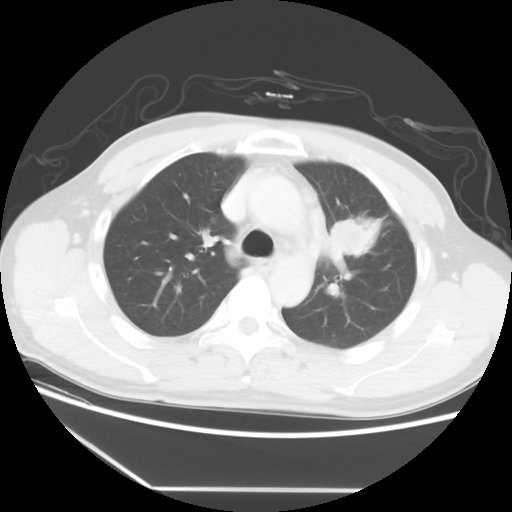
Chest CT, one axial slice. Slice 39 of 56 in the series (ordered by position). 120 kVp. Lung window (W 1500 / L -600 HU). 5 mm slice thickness. 512 × 512 image matrix, field of view 373 × 373 mm. Male patient, age 53 years. From the clinical record (not read from this slice): clinical TNM (as recorded): T2a N1 M1b.
Annotated regions visible in this slice (rectangle marked by the reading radiologist):
- lung tumour (recorded histology: adenocarcinoma): bounding box (x1, y1, x2, y2) in pixels: (322, 206, 386, 263)